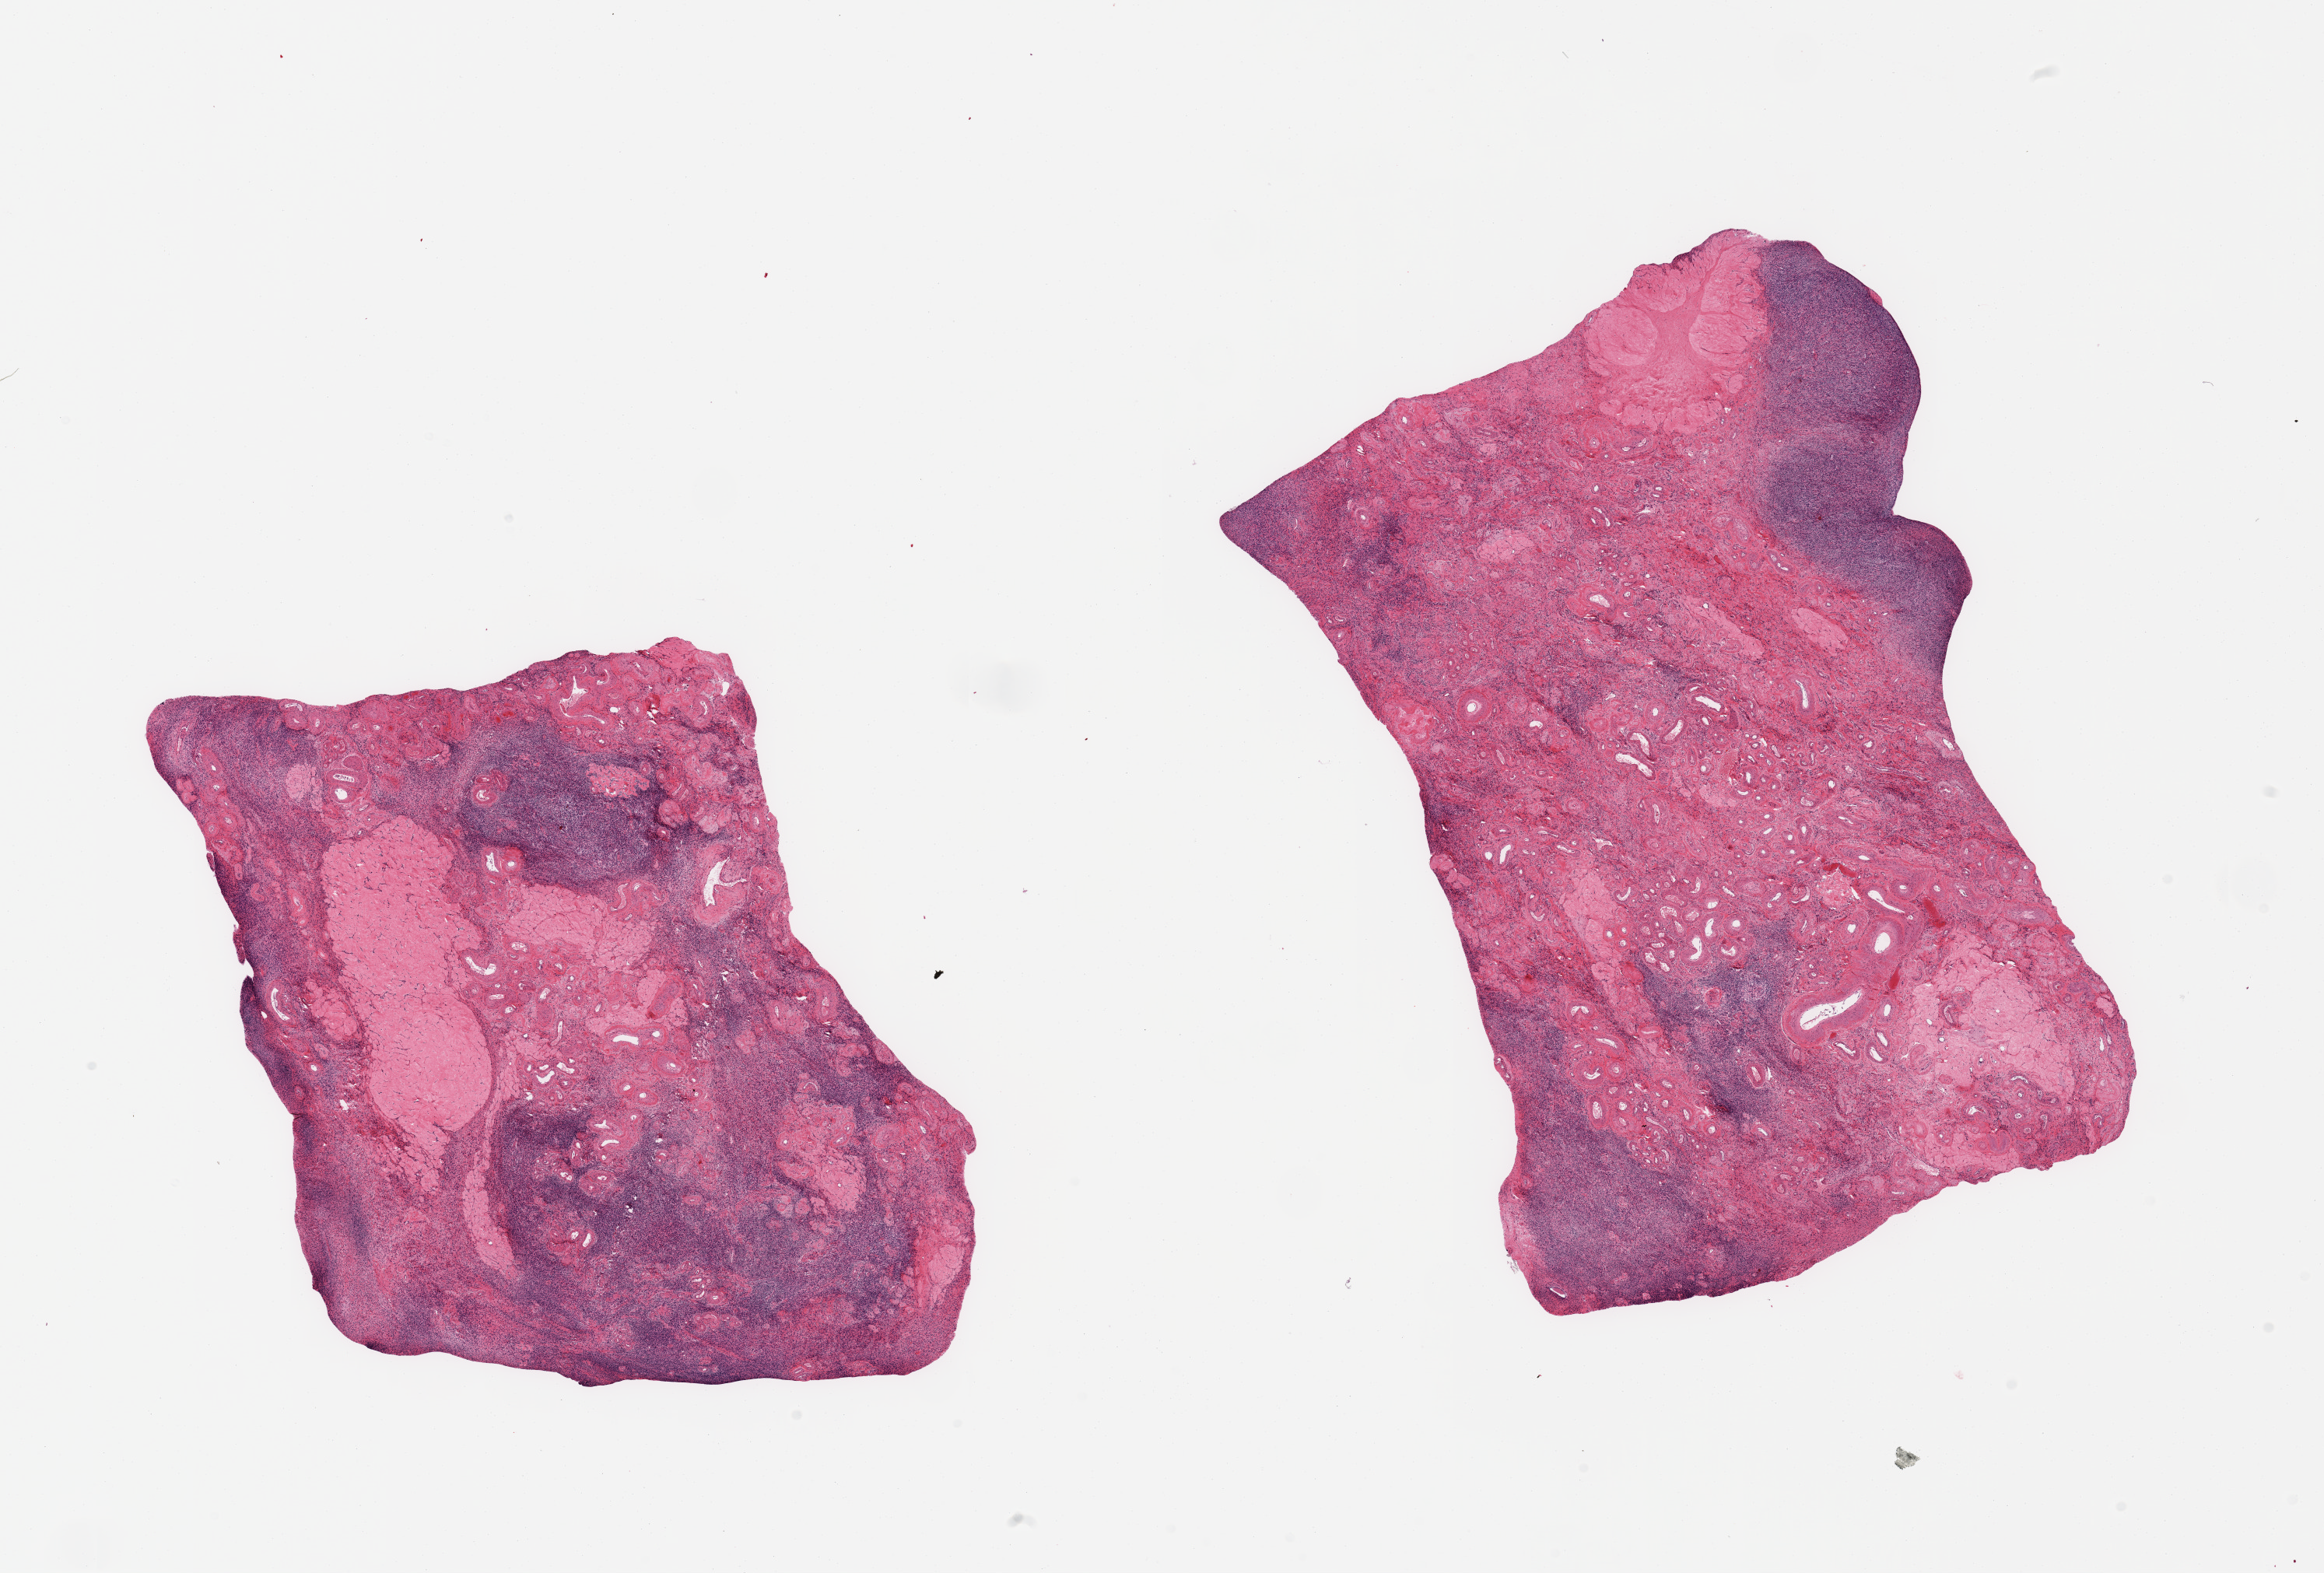
Whole-slide image, H&E stain, a low-resolution overview of the entire scanned area, about 23.6 x 16.0 mm; PAXgene-fixed, paraffin-embedded tissue; section of ovary (target tissue); donor tissue sample.
Reviewer comment on this tissue sample: 2 pieces; parenchyma comprises 25%, remainder mostly corpora albicantia and vascularized stroma.